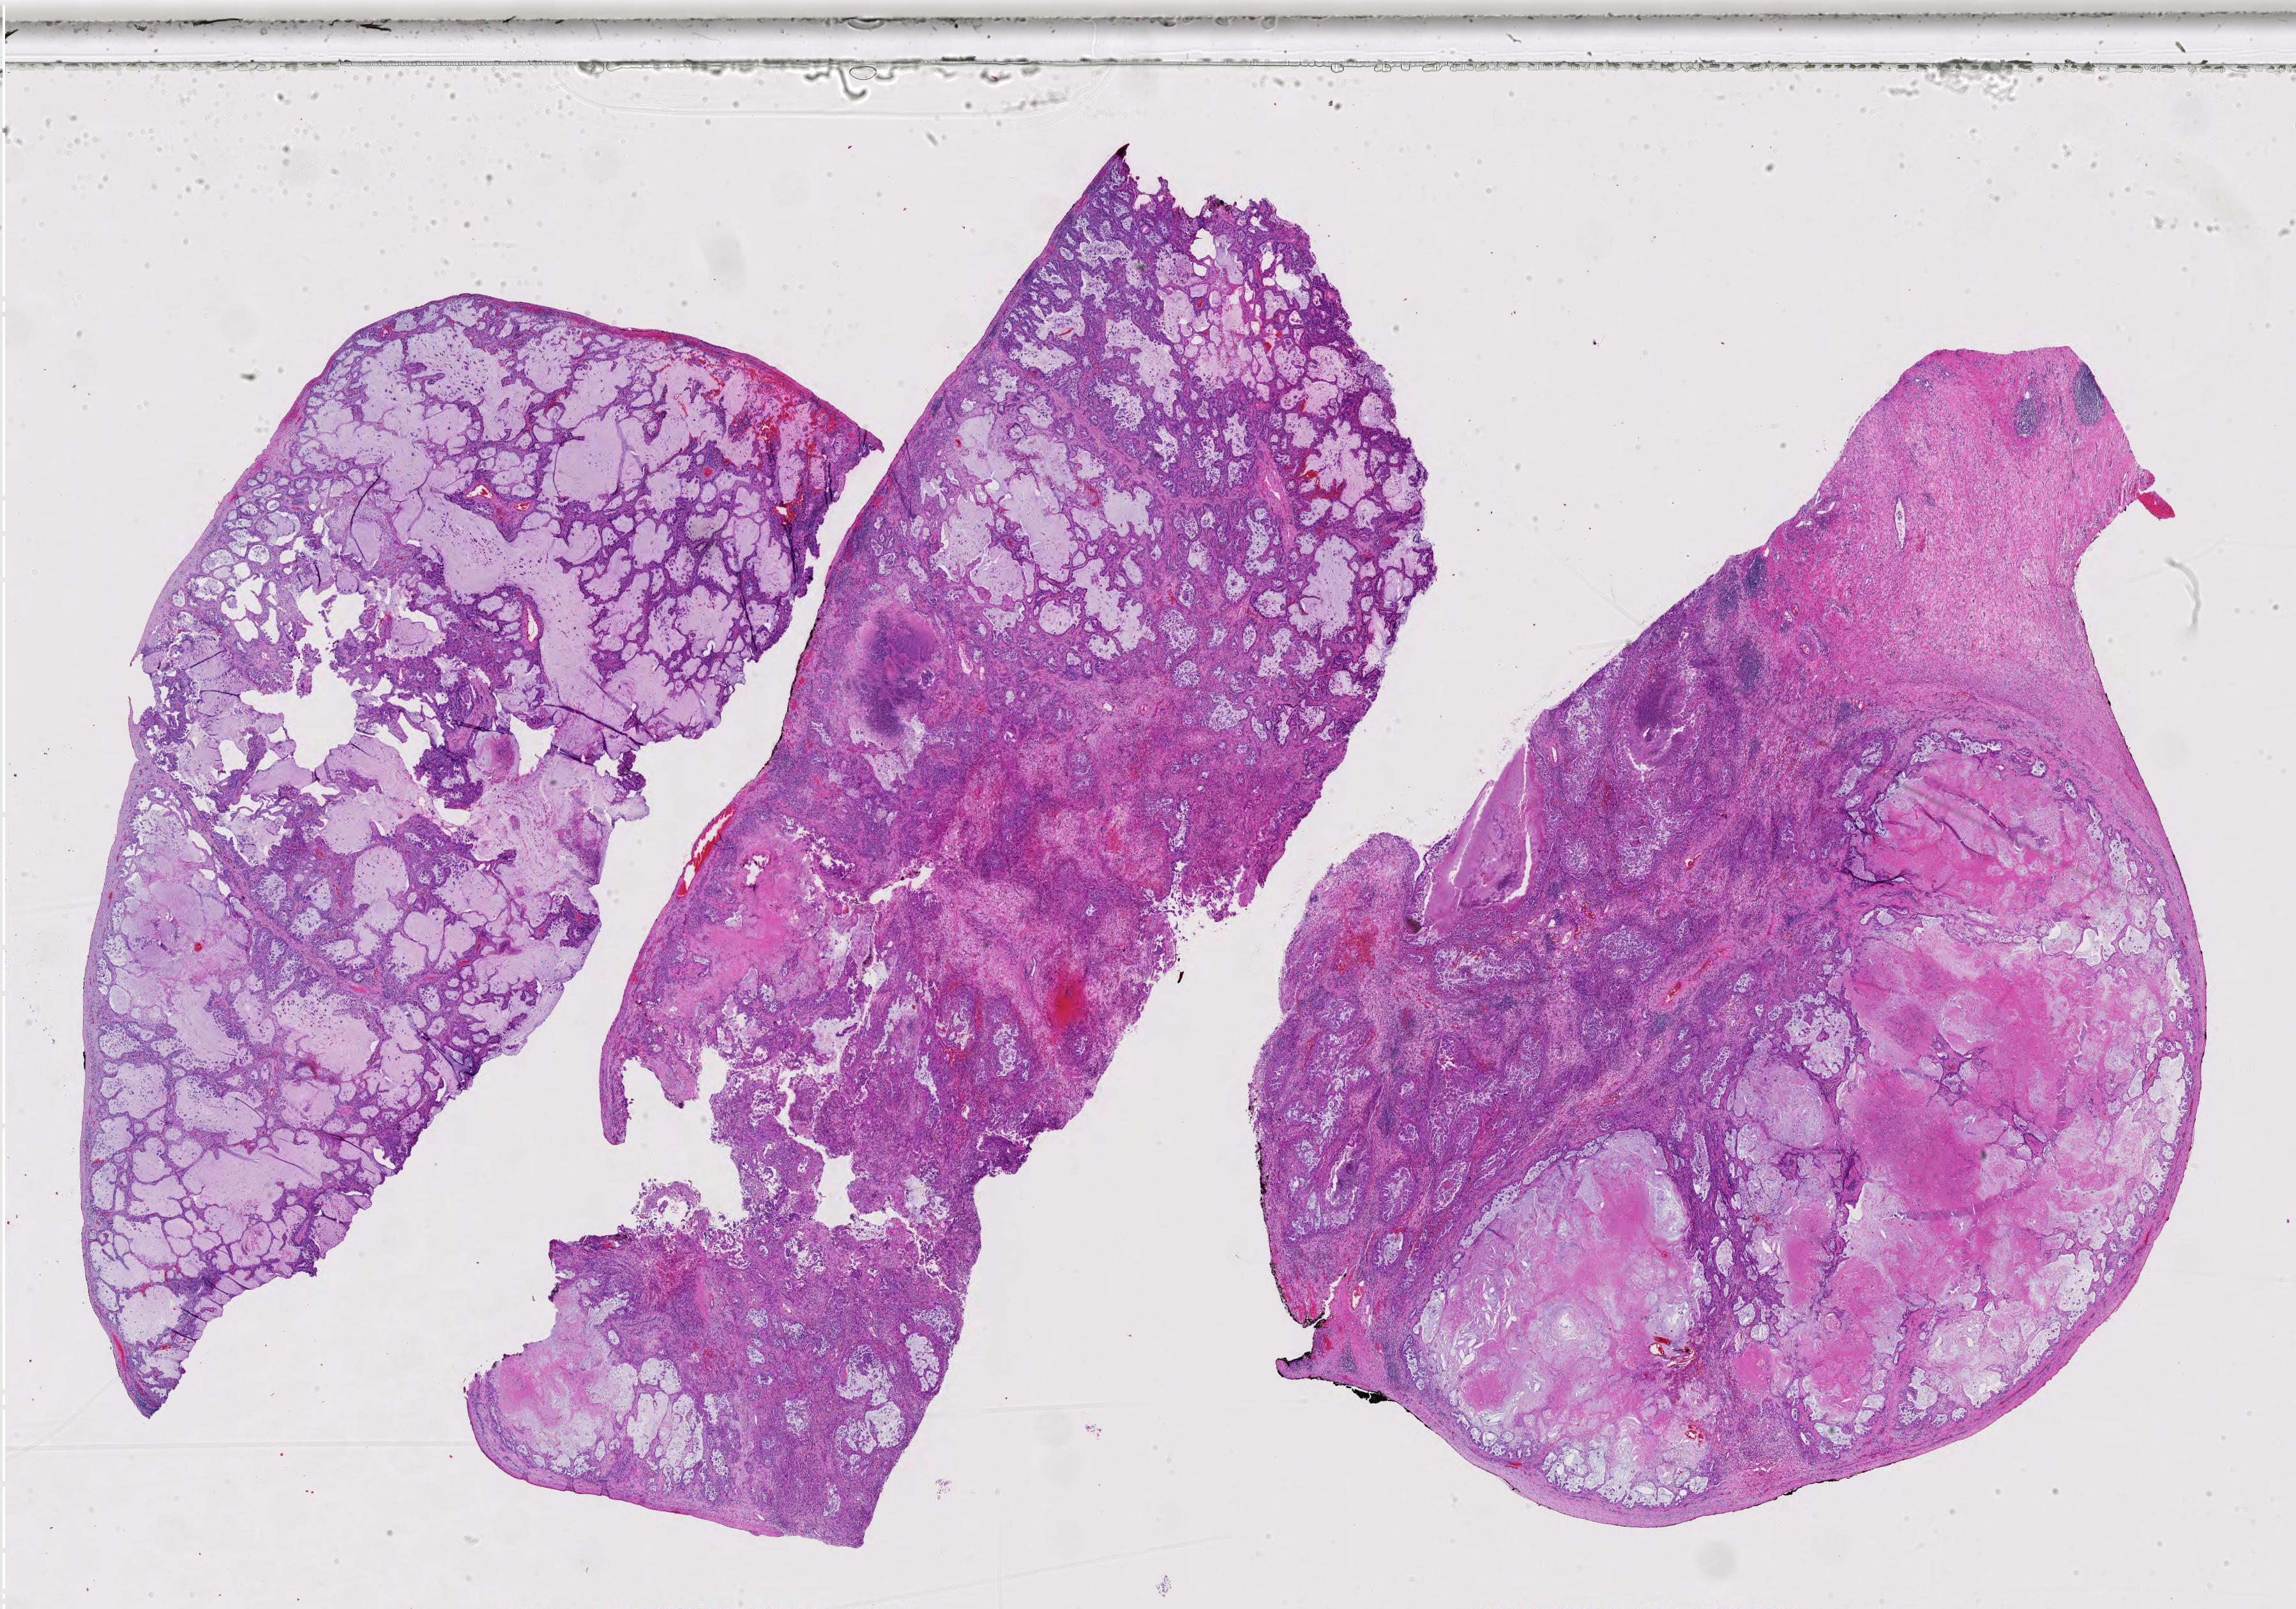
Digitized H&E-stained tissue section (whole slide) — shown as a low-resolution overview of the whole scanned area (about 26.1 x 18.3 mm, slide scanned at 40x); formalin-fixed paraffin-embedded (FFPE) diagnostic section; sample: primary tumour, lung. Female patient; age at initial diagnosis 74 years.
- pathologic diagnosis: Adenocarcinoma with mixed subtypes (upper lobe, lung)
- AJCC pathologic stage: IIIA (7th edition)